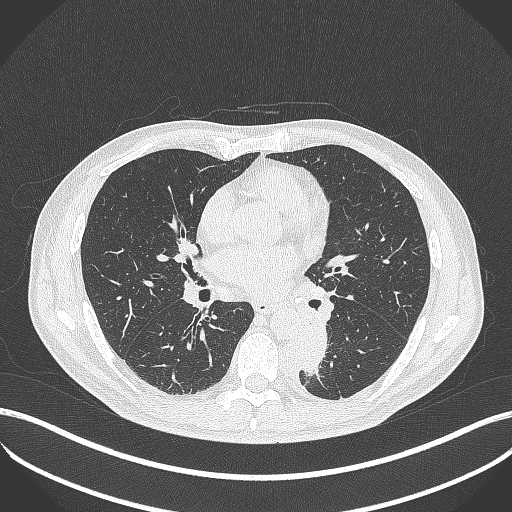
Chest CT, one axial slice; position 205 of 451 along the scan axis; reconstruction kernel B70f; lung window (W 1500 / L -600 HU); 1 mm slice thickness; 512 × 512 image matrix. Male patient, age 72 years. Case-level facts recorded for this patient, not image findings: clinical TNM (as recorded): T2b N0 M1.
Structures marked on this image (rectangle marked by the reading radiologist):
- lung tumour (recorded histology: adenocarcinoma): box from (x=285, y=316) to (x=332, y=389) px